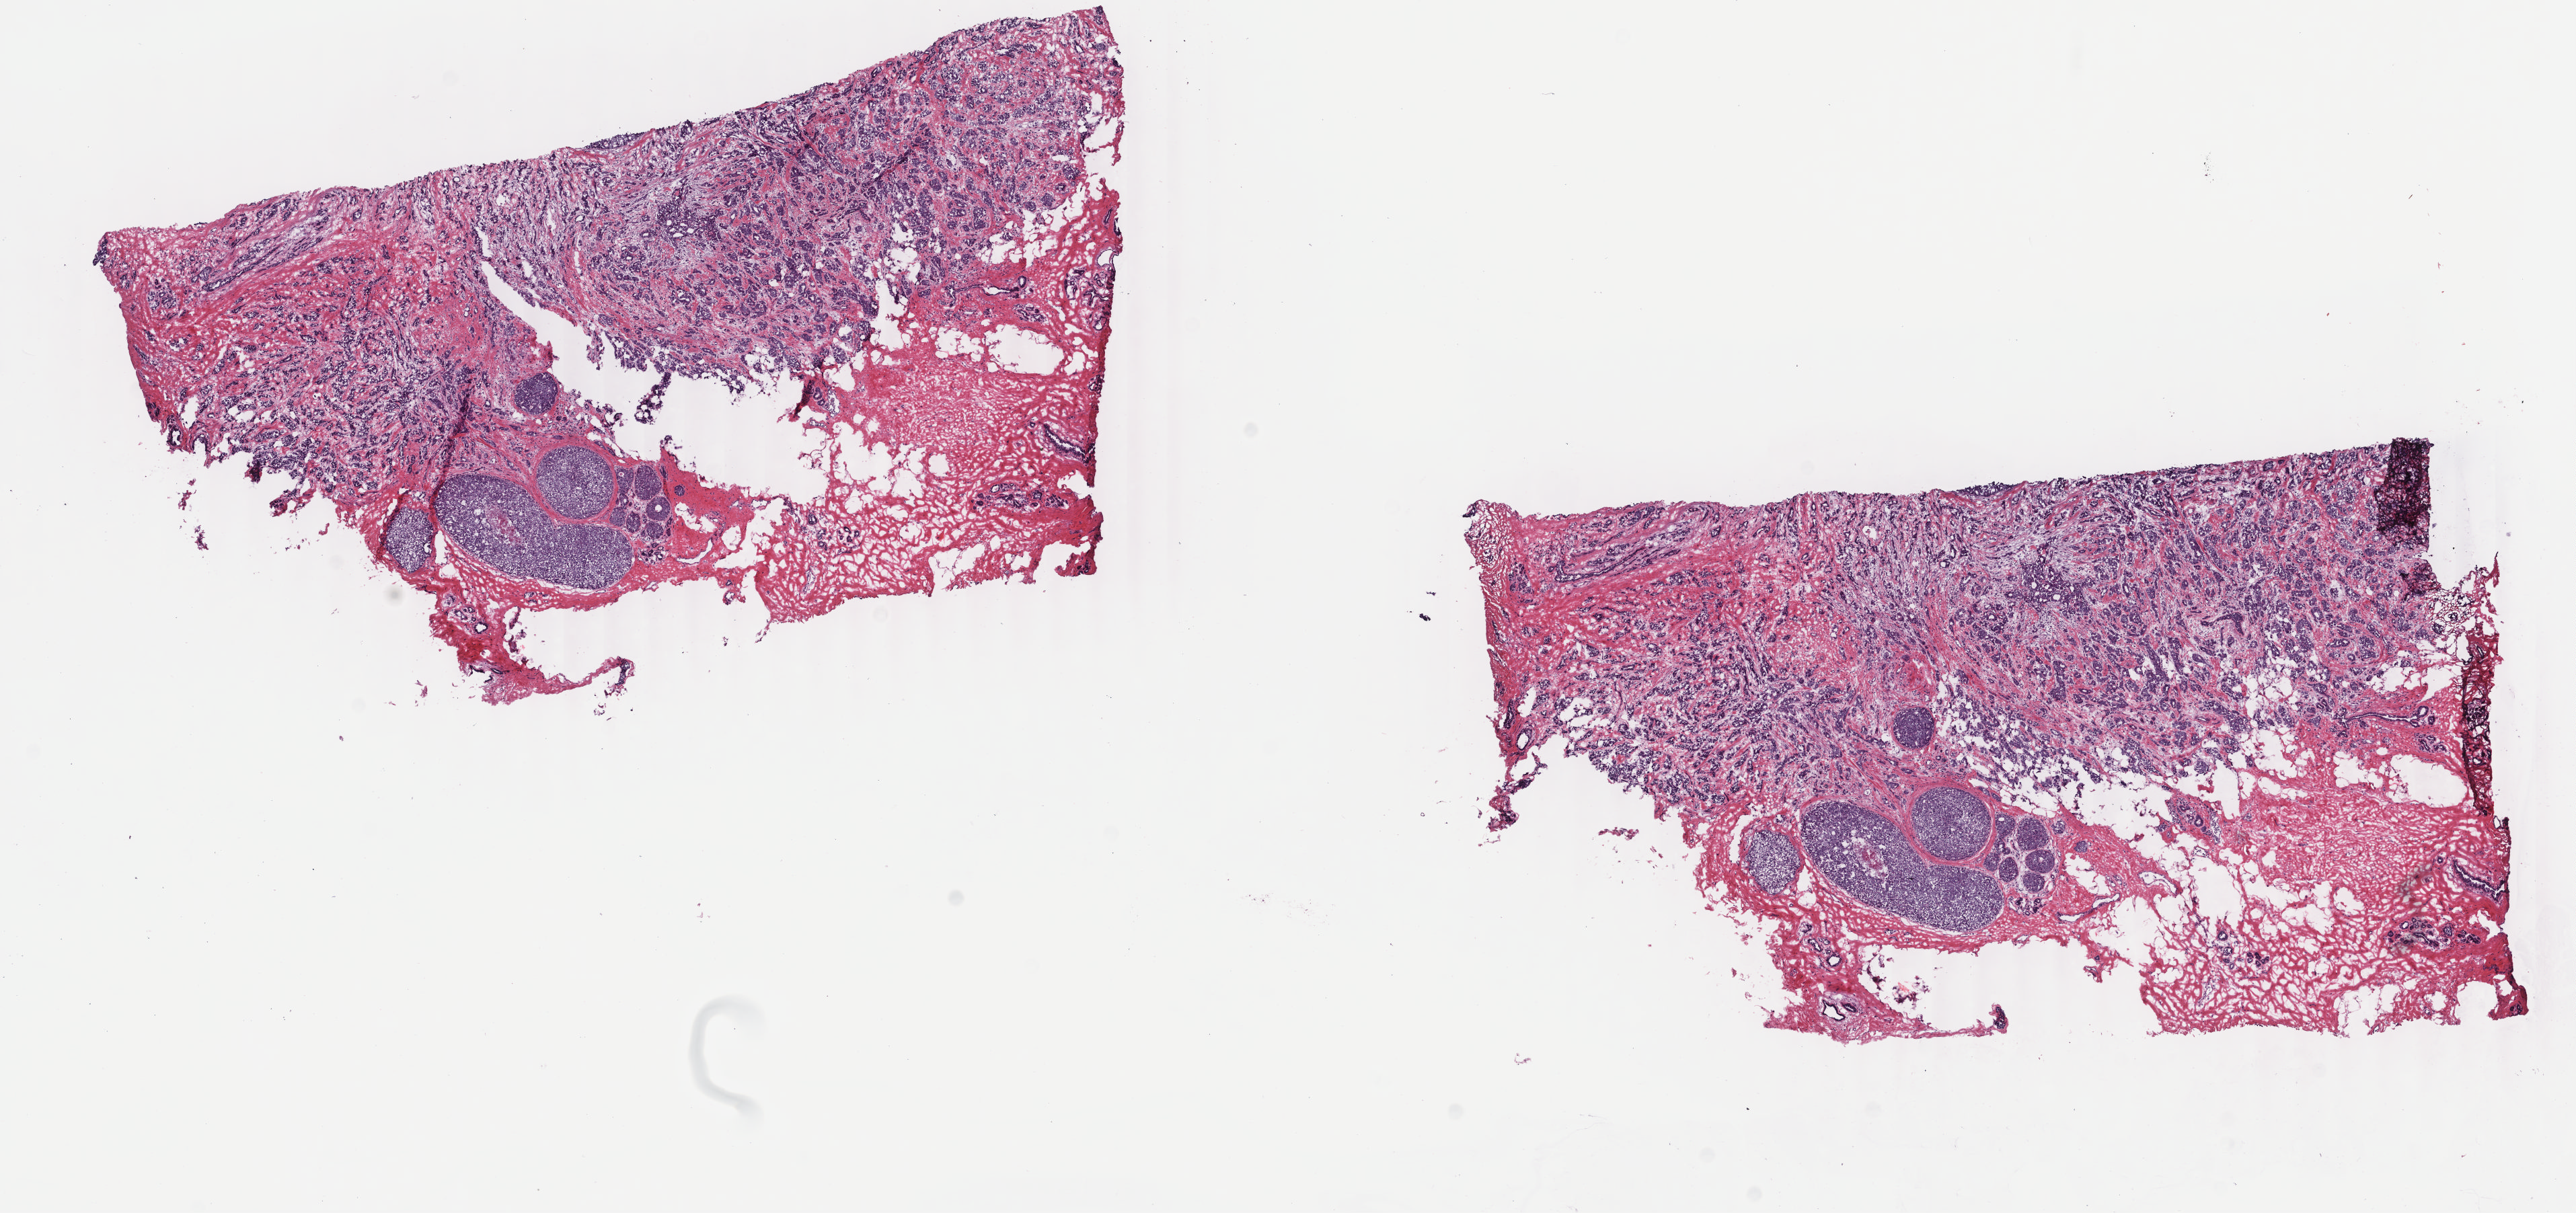
Hematoxylin and eosin (H&E) stained whole-slide image, low-resolution overview of the scanned area, about 15.2 x 7.2 mm. Frozen section from the top of the tissue portion. Sample: primary tumour, breast. Female, age 55 years at initial diagnosis.
Diagnosis: Infiltrating duct carcinoma, NOS.